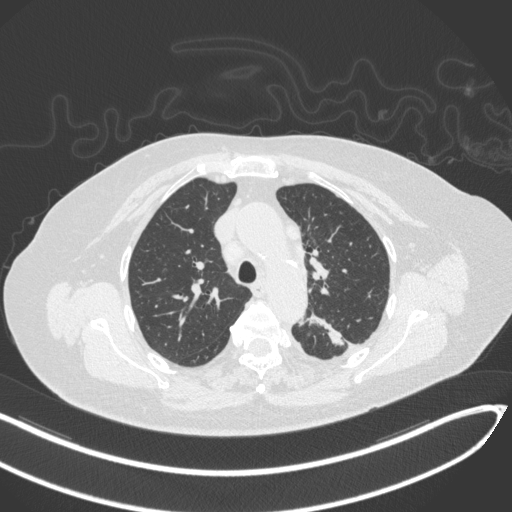
Chest CT, one axial slice; position 225 of 270 along the scan axis; lung window (W 1500 / L -600 HU); 1 mm slice thickness; 512 × 512 image matrix. Female patient, age 76 years. From the clinical record (not read from this slice): clinical TNM (as recorded): T1c N0 M0.
Annotated regions visible in this slice (rectangle marked by the reading radiologist):
- lung tumour (recorded histology: adenocarcinoma): box from (x=307, y=311) to (x=351, y=353) px